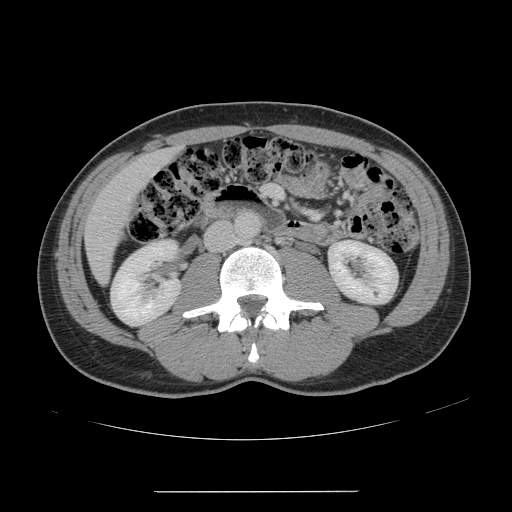
Contrast-enhanced abdominal CT, one axial slice. Position 43 of 178 along the scan axis. 120 kVp. Intravenous contrast given. Soft-tissue window (W 400 / L 40 HU). 2.5 mm slice thickness. 512 × 512 image matrix, field of view 401 × 401 mm. Male patient, age 53 years. From the clinical record (not read from this slice): diagnosis: colorectal cancer liver metastases, imaged before liver resection; multiple liver metastases: yes; largest metastasis: 2.4 cm; disease in both lobes: no.
Structures marked on this image (outlined manually by an expert reader):
- hepatic veins: box from (x=97, y=171) to (x=155, y=259) px
- liver: (x=85, y=149)–(x=176, y=283)